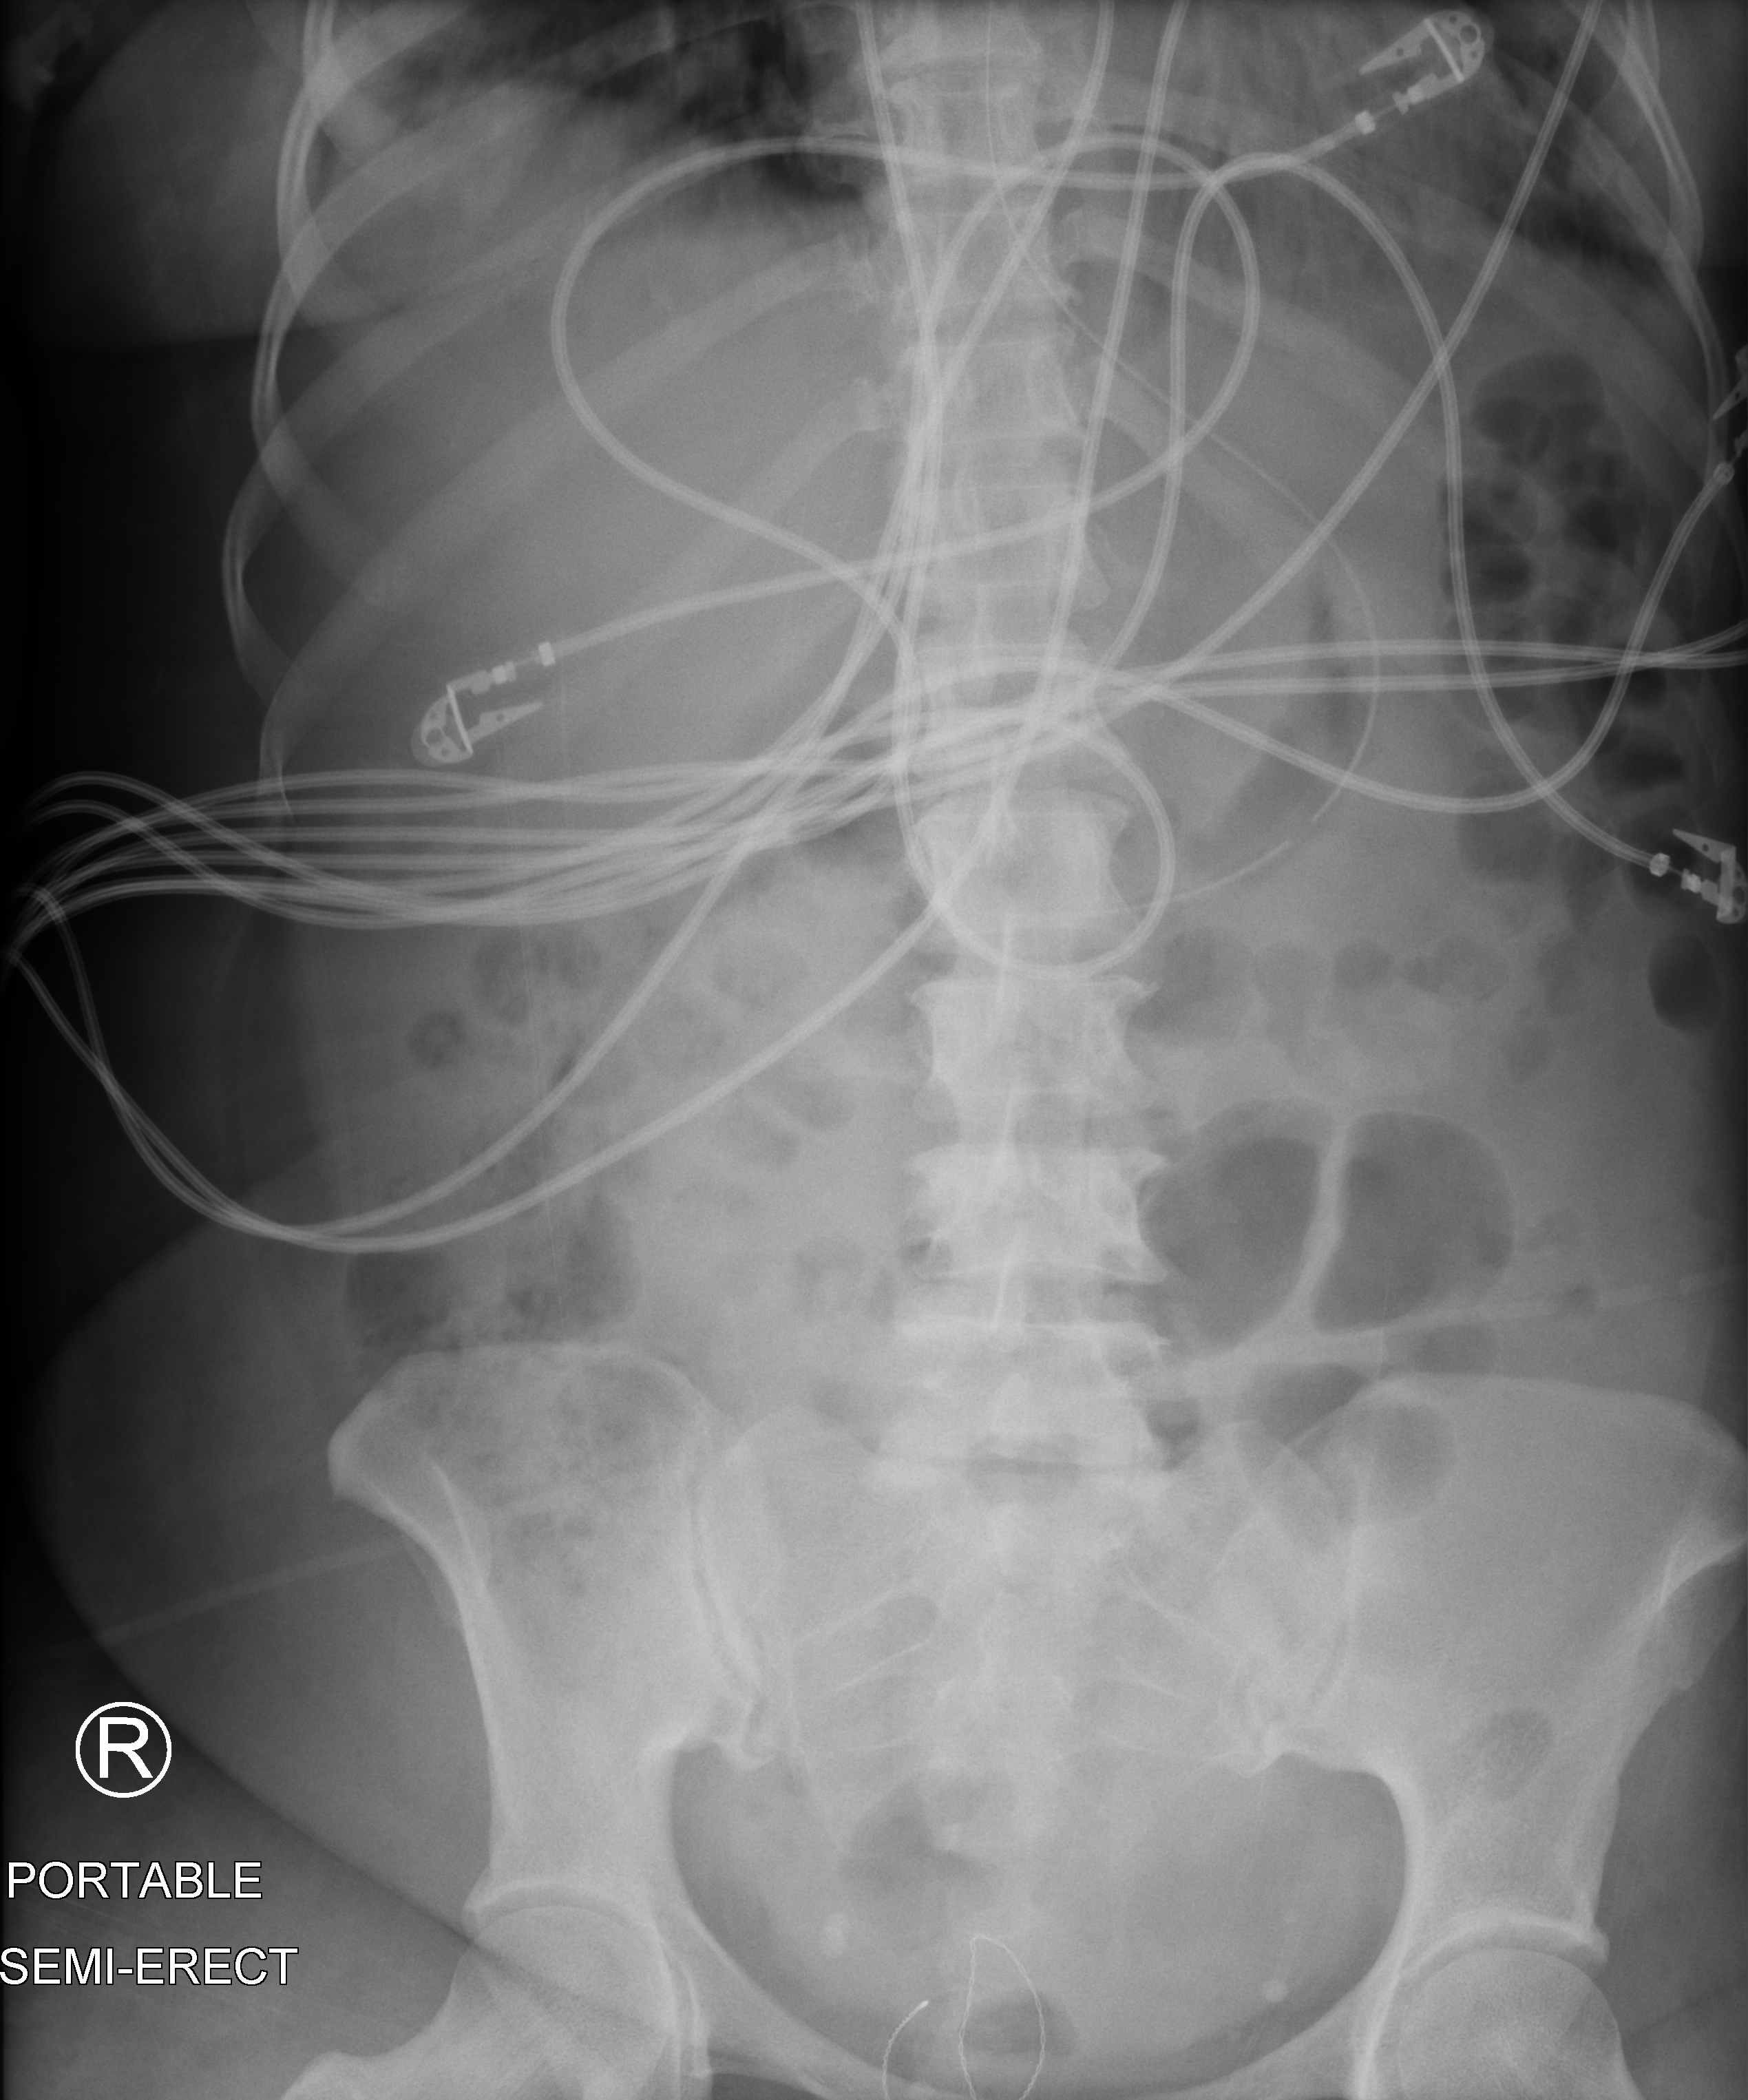
Abdomen X-ray (portable), anteroposterior (AP) projection. Female patient hospitalised with COVID-19, age 18–59 years.
Hospital-stay facts (about this admission, not read from this image; timing relative to this image not recorded): diabetes (admission record): no; mechanically ventilated during this hospital stay: yes.